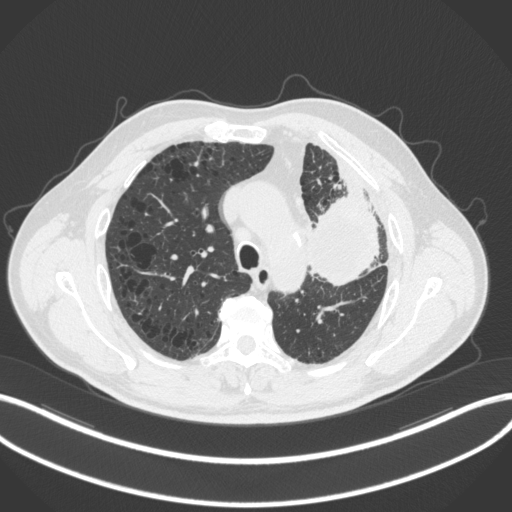
Chest CT, one axial slice. Position 212 of 286 along the scan axis. Reconstruction kernel B31f. Lung window (W 1500 / L -600 HU). 512 × 512 image matrix, field of view 400 × 400 mm. Male patient, age 68 years. Case-level facts recorded for this patient, not image findings: clinical TNM (as recorded): T3 N3 M1.
Annotated regions visible in this slice (bounding box drawn by a radiologist):
- lung tumour (recorded histology: adenocarcinoma): bounding box [x1, y1, x2, y2] px = [301, 186, 383, 293]